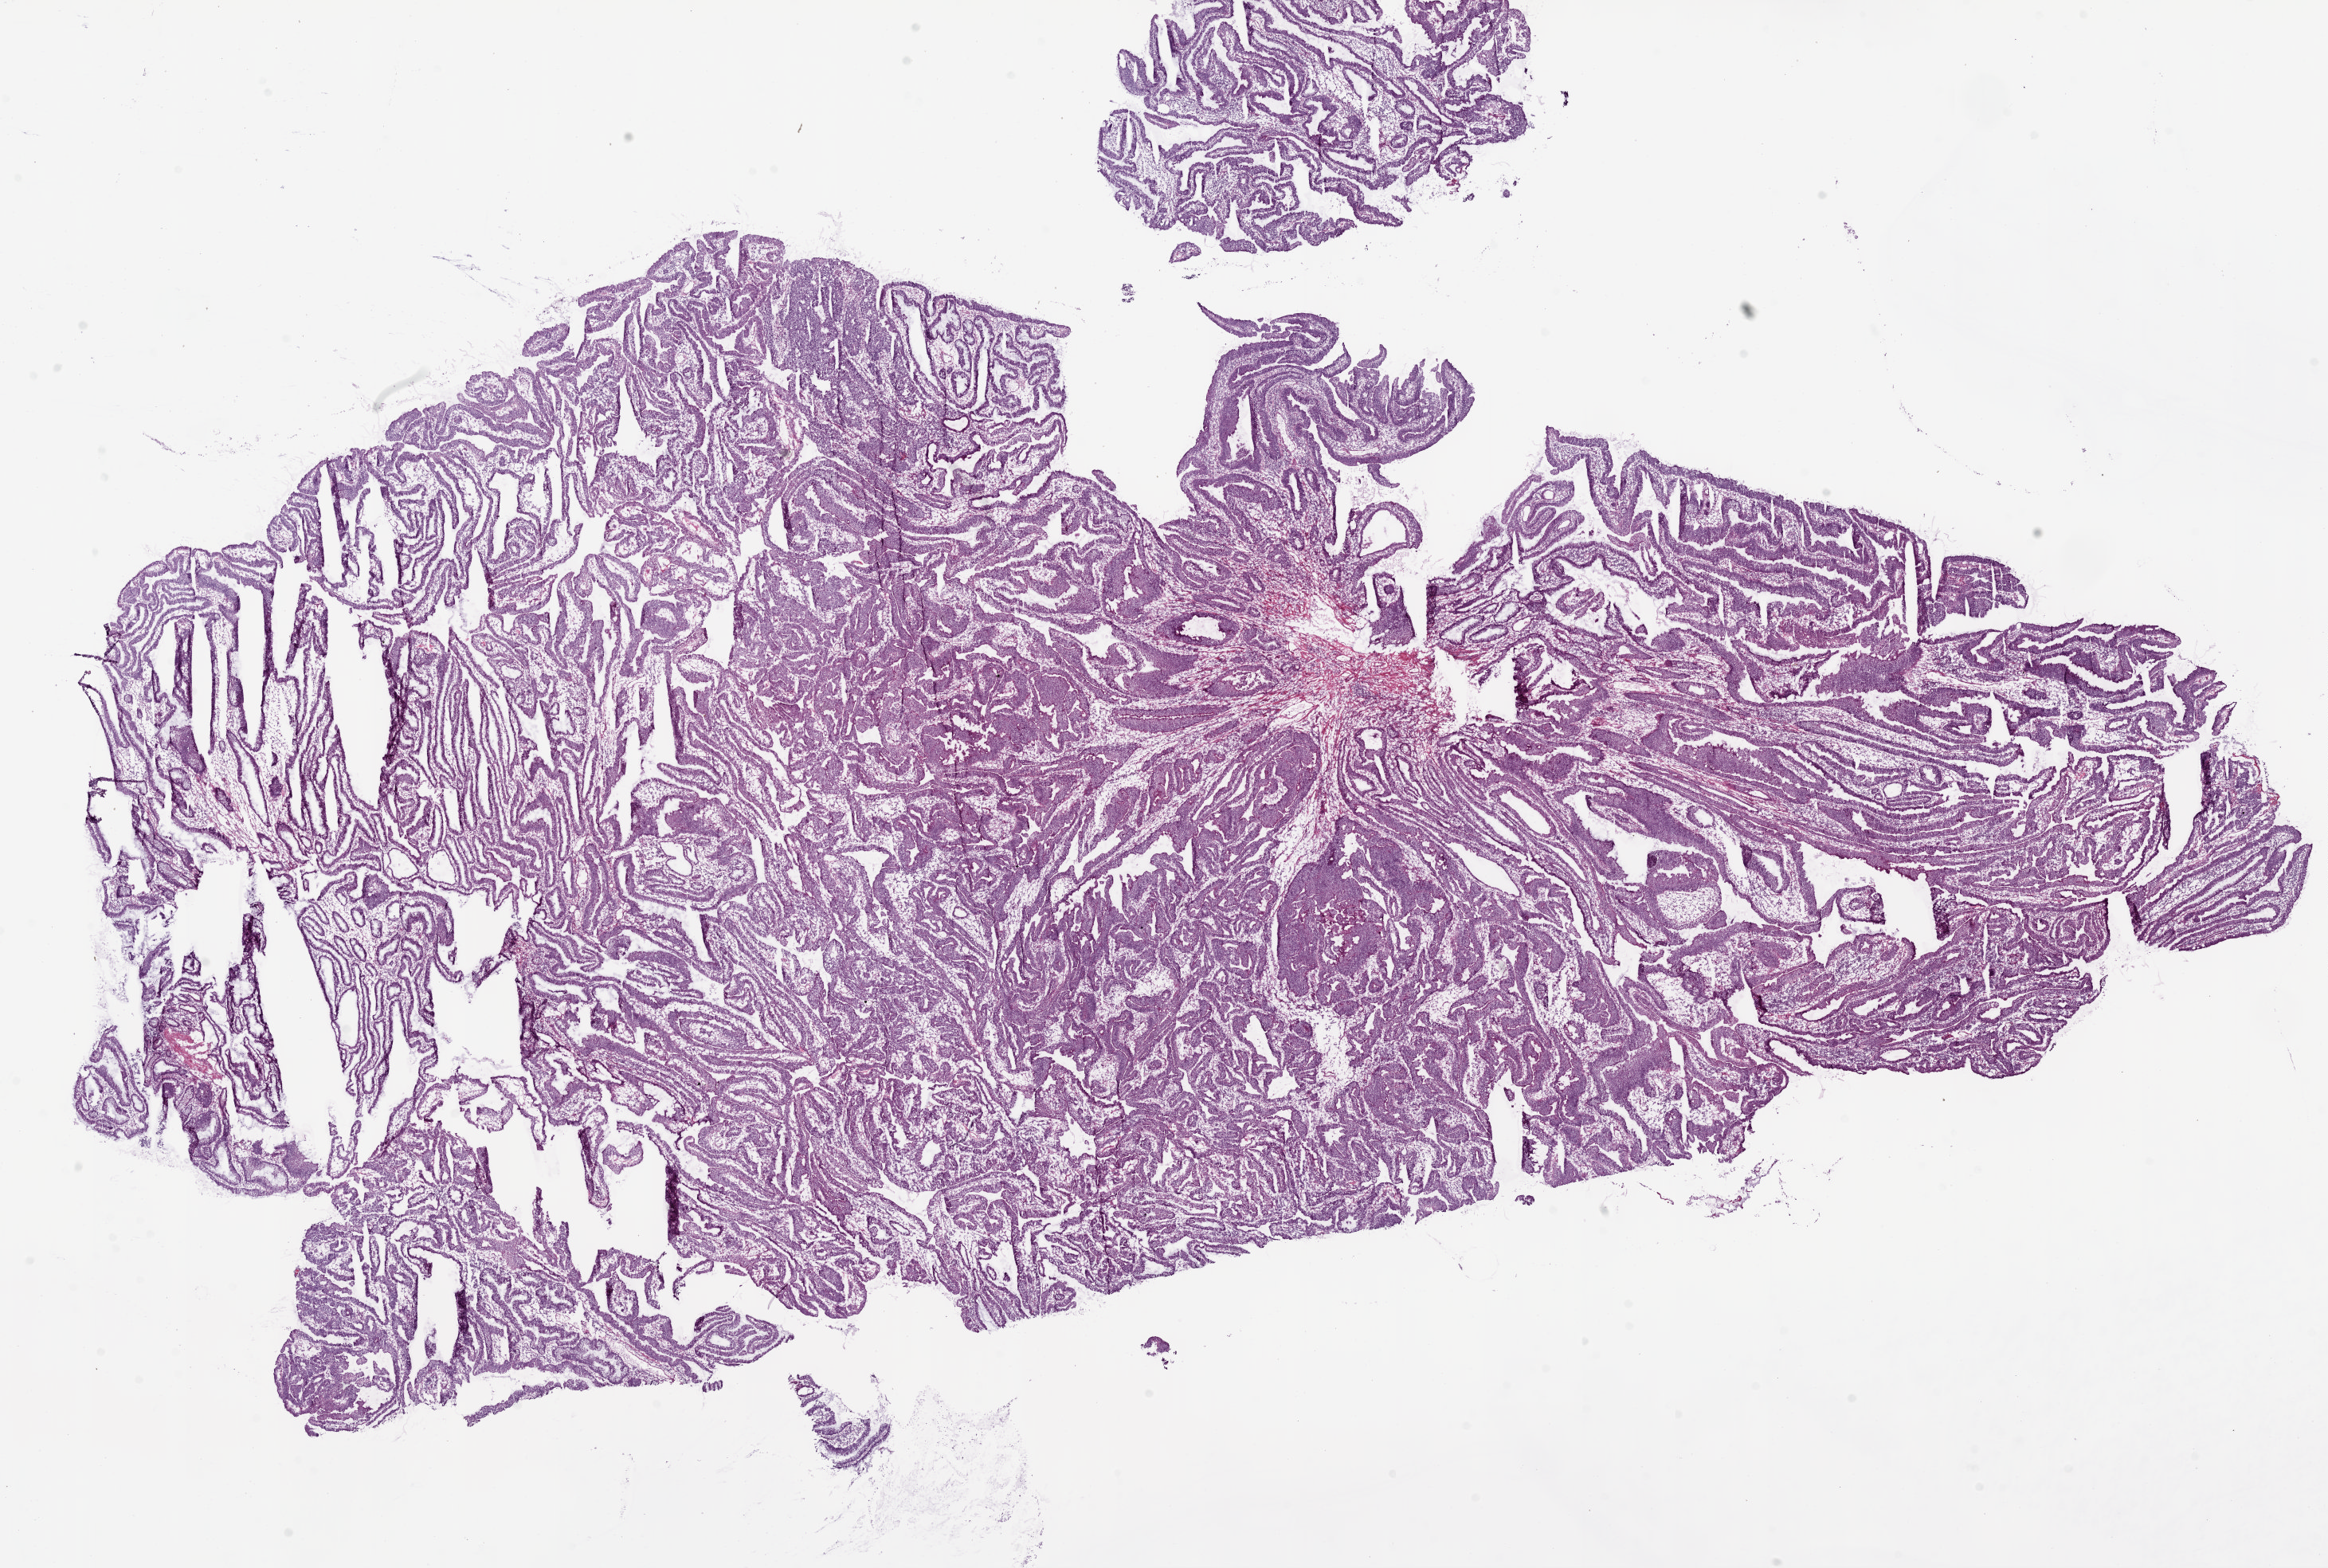
Whole-slide histology image, H&E-stained — shown as a low-resolution overview of the whole scanned area (about 23.4 x 15.8 mm, slide scanned at 5x). Frozen section from the bottom of the tissue portion. Primary tumour sample from the colon. Female patient; age at initial diagnosis 51 years. Slide review estimates, as recorded: tumour cells 75%, tumour nuclei 75%, normal cells 15%, stromal cells 10%, necrosis 0%.
Pathologic diagnosis: Adenocarcinoma, NOS (cecum). AJCC pathologic stage: I (6th edition).